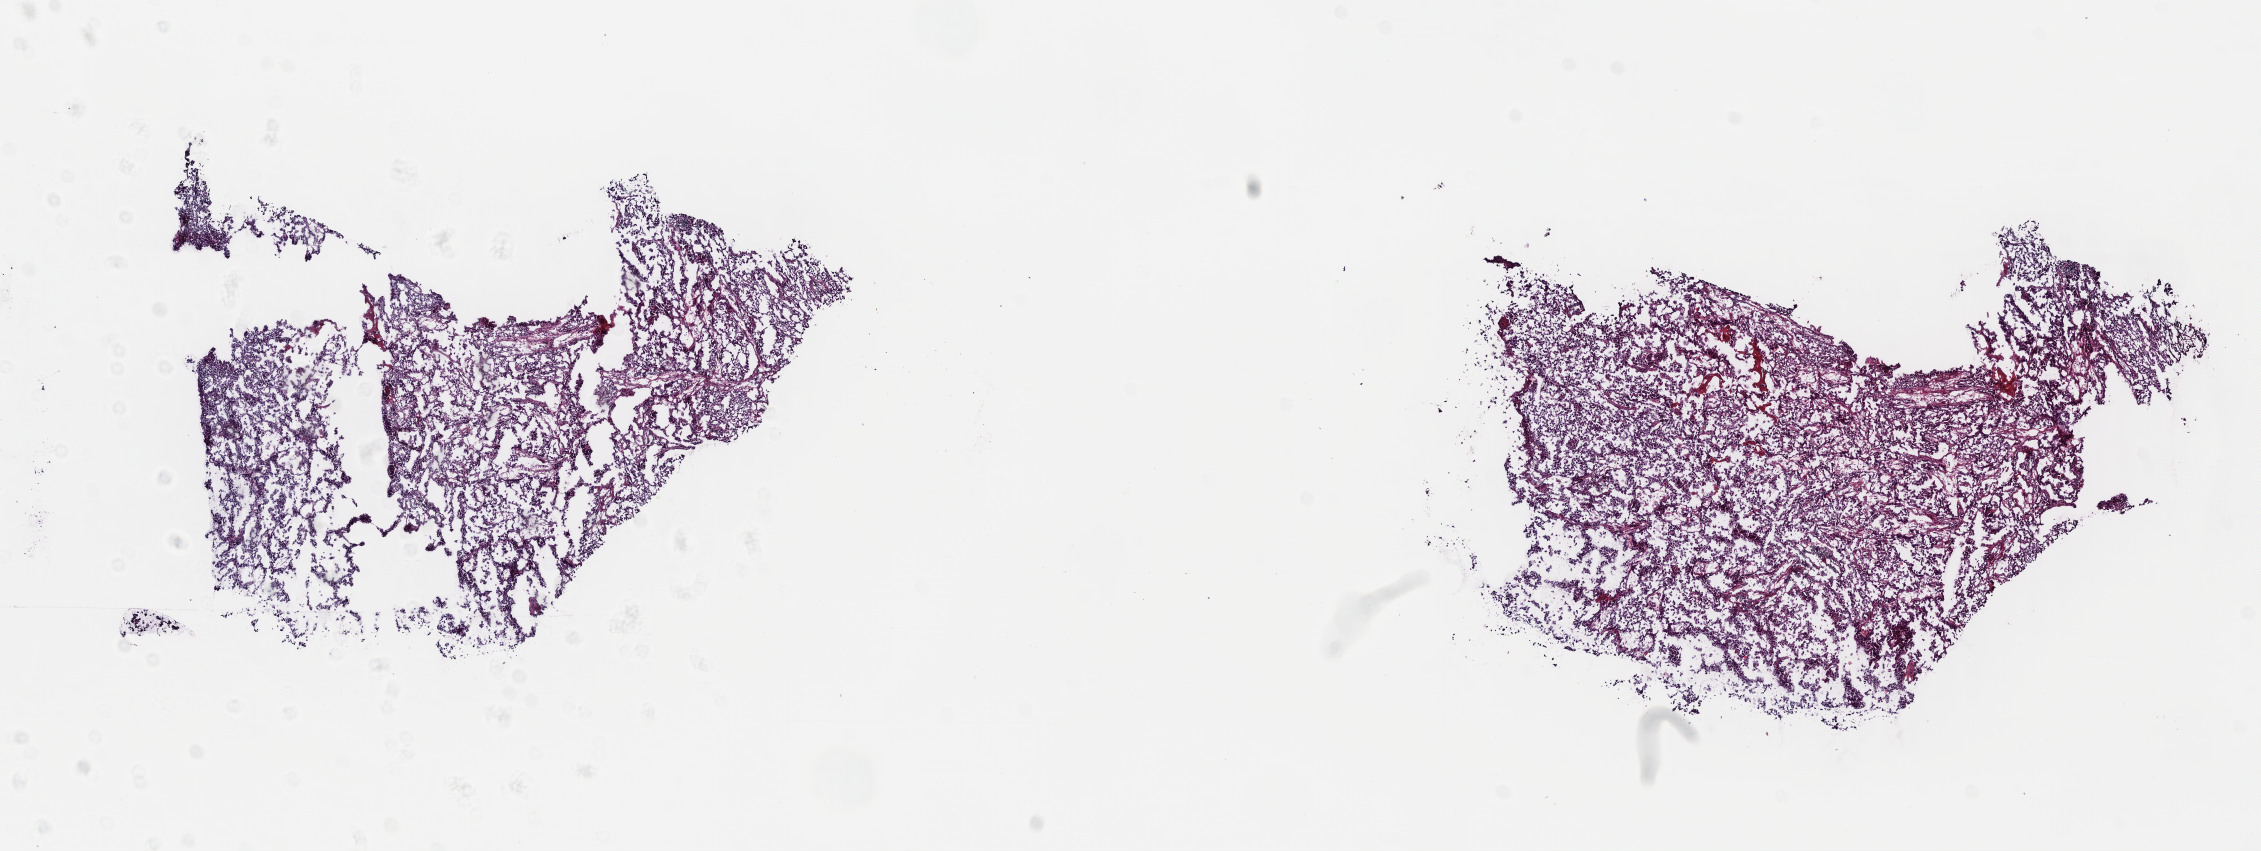
H&E whole-slide image, shown as a low-resolution overview of the whole scanned area (about 17.8 x 6.7 mm), frozen section from the top of the tissue portion, bladder, primary tumour sample. Male patient; age at initial diagnosis 66 years. Histologic grade: high grade. Slide review estimates, as recorded: tumour cells 100%, tumour nuclei 80%, normal cells 0%, stromal cells 0%, necrosis 0%. Infiltration values recorded for this section: lymphocyte infiltration 2%, monocyte infiltration 0%, neutrophil infiltration 0%.
- diagnosis: Papillary transitional cell carcinoma
- AJCC pathologic stage: II (7th edition)